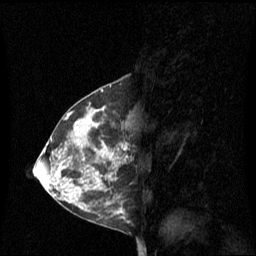
Breast MRI (dynamic contrast-enhanced), one sagittal slice; dynamic contrast-enhanced series, image 2 of 3 at this slice position (ordered by acquisition); 1.5 T; TE 4.2 ms, TR 8.4 ms; 256 × 256 image matrix, field of view 240 × 240 mm. Patient: female, 42 years. Case-level facts recorded for this patient, not image findings: setting: breast cancer imaged before/during neoadjuvant chemotherapy; receptor status: HR-positive, HER2-negative.
Structures marked on this image (semi-automatic segmentation, software-assisted and operator-edited):
- analysis volume of interest (the breast-tissue region the enhancement analysis was run in; not a lesion): bounding box [x1, y1, x2, y2] px = [68, 108, 129, 201]
- tumour enhancement mask (voxels above the 70 % enhancement threshold inside the analysis volume of interest): [90, 110, 127, 159]